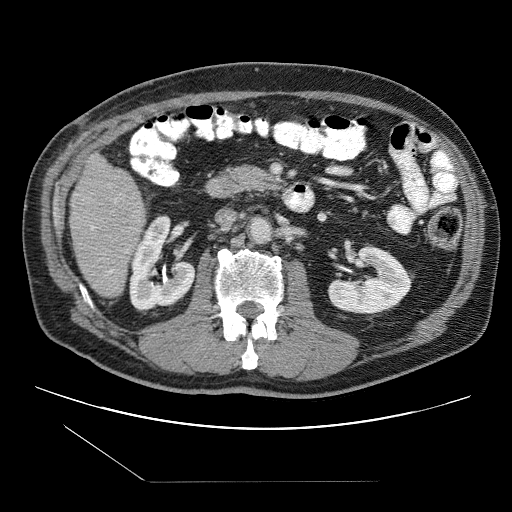
Contrast-enhanced abdominal CT (liver protocol), one axial slice; slice 29 of 109 in the series (ordered by position); reconstruction kernel STANDARD; 120 kVp; one of 2 acquisitions stored at this slice position; soft-tissue window (W 400 / L 40 HU); 2.5 mm slice thickness; 512 × 512 image matrix. From the clinical record (not read from this slice): diagnosis: hepatocellular carcinoma (patient treated with transarterial chemoembolisation; whether this scan precedes or follows treatment is not stated here); TNM stage (as recorded): Stage-IIIB; Child-Pugh class: A.
Outlined on this slice (semi-automatically segmented with operator editing):
- liver parenchyma outside the tumour (the mass and vessels are separate outlines, so this box may not span the whole liver): bounding box (x1, y1, x2, y2) in pixels: (69, 152, 146, 296)
- liver vessels: (91, 226, 113, 273)